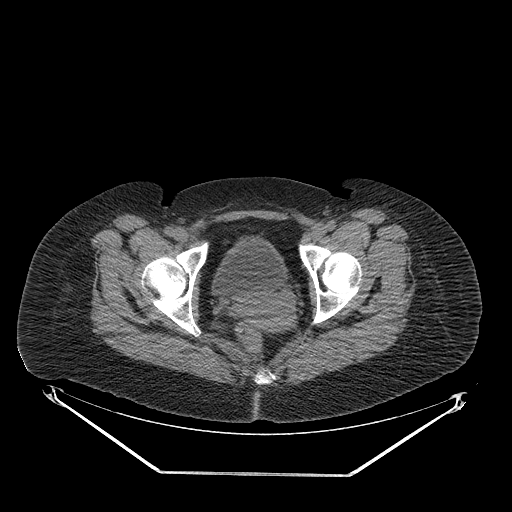
CT of an extremity soft-tissue mass (from a PET/CT study), one axial slice. Position 61 of 267 along the scan axis. 140 kVp. Soft-tissue window (W 400 / L 40 HU). 512 × 512 image matrix, field of view 500 × 500 mm. Female patient. From the clinical record (not read from this slice): histological type: myxofibrosarcoma; grade: intermediate; site of the primary tumour: left thigh.
Outlined on this slice (expert contour drawn on MRI and transferred to this co-registered scan by the dataset authors):
- gross tumour volume including surrounding oedema: bounding box <306,228,330,250> (left, top, right, bottom; pixels)